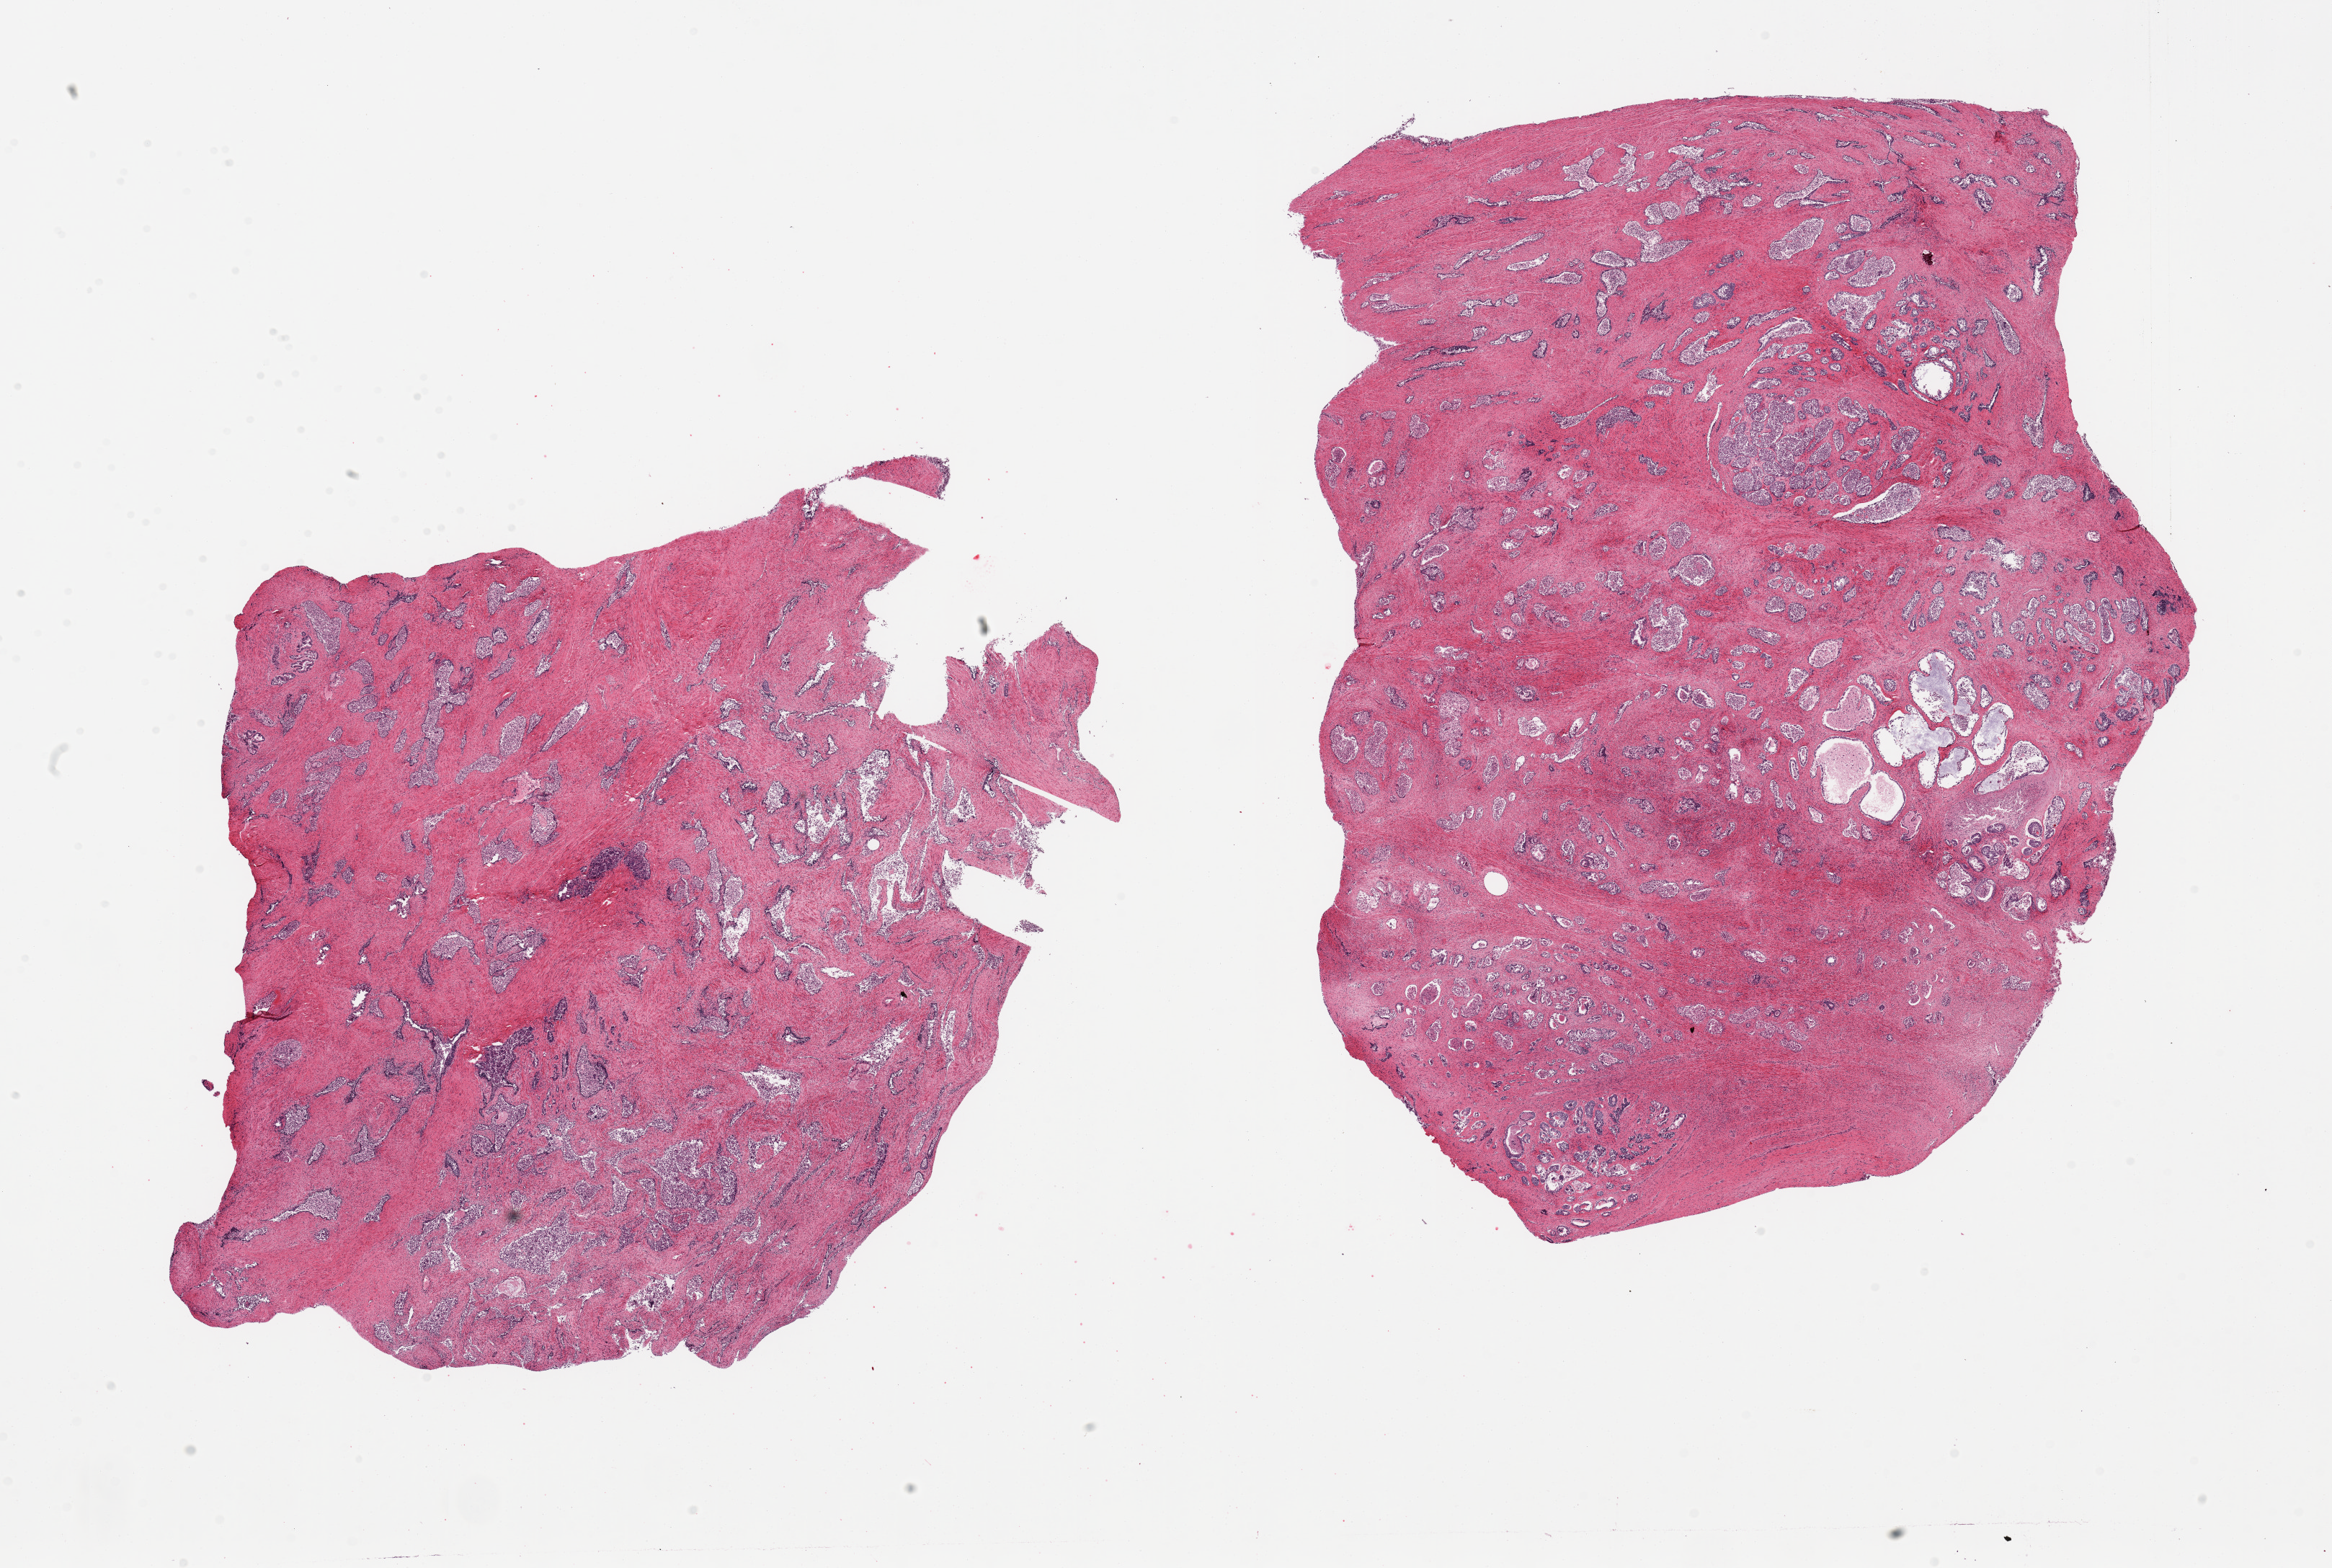
Digitized haematoxylin and eosin-stained section, brightfield, shown as a low-resolution overview of the whole scanned area (about 25.6 x 17.2 mm); PAXgene-fixed, paraffin-embedded tissue; target tissue: prostate; tissue donor sample. Donor: male.
* reviewer comment on this tissue sample: 2 pieces, hyperplastic glandular pattern; glandular epithelium with moderate-advanced autolysis